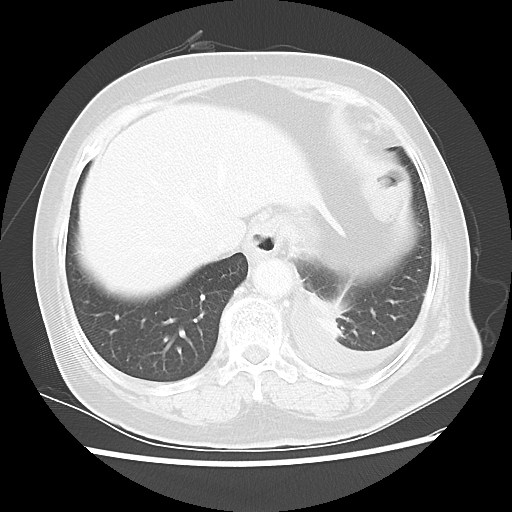
Chest CT, one axial slice; slice 5 of 40 in the series (ordered by position); reconstruction kernel LUNG; 100 kVp; lung window (W 1500 / L -600 HU); 5 mm slice thickness; 512 × 512 image matrix, field of view 343 × 343 mm. Female patient, age 68 years. Case-level facts recorded for this patient, not image findings: clinical TNM (as recorded): T1c N0 M1.
Annotated regions visible in this slice (bounding box drawn by a radiologist):
- lung tumour (recorded histology: adenocarcinoma): box from (x=308, y=292) to (x=348, y=343) px